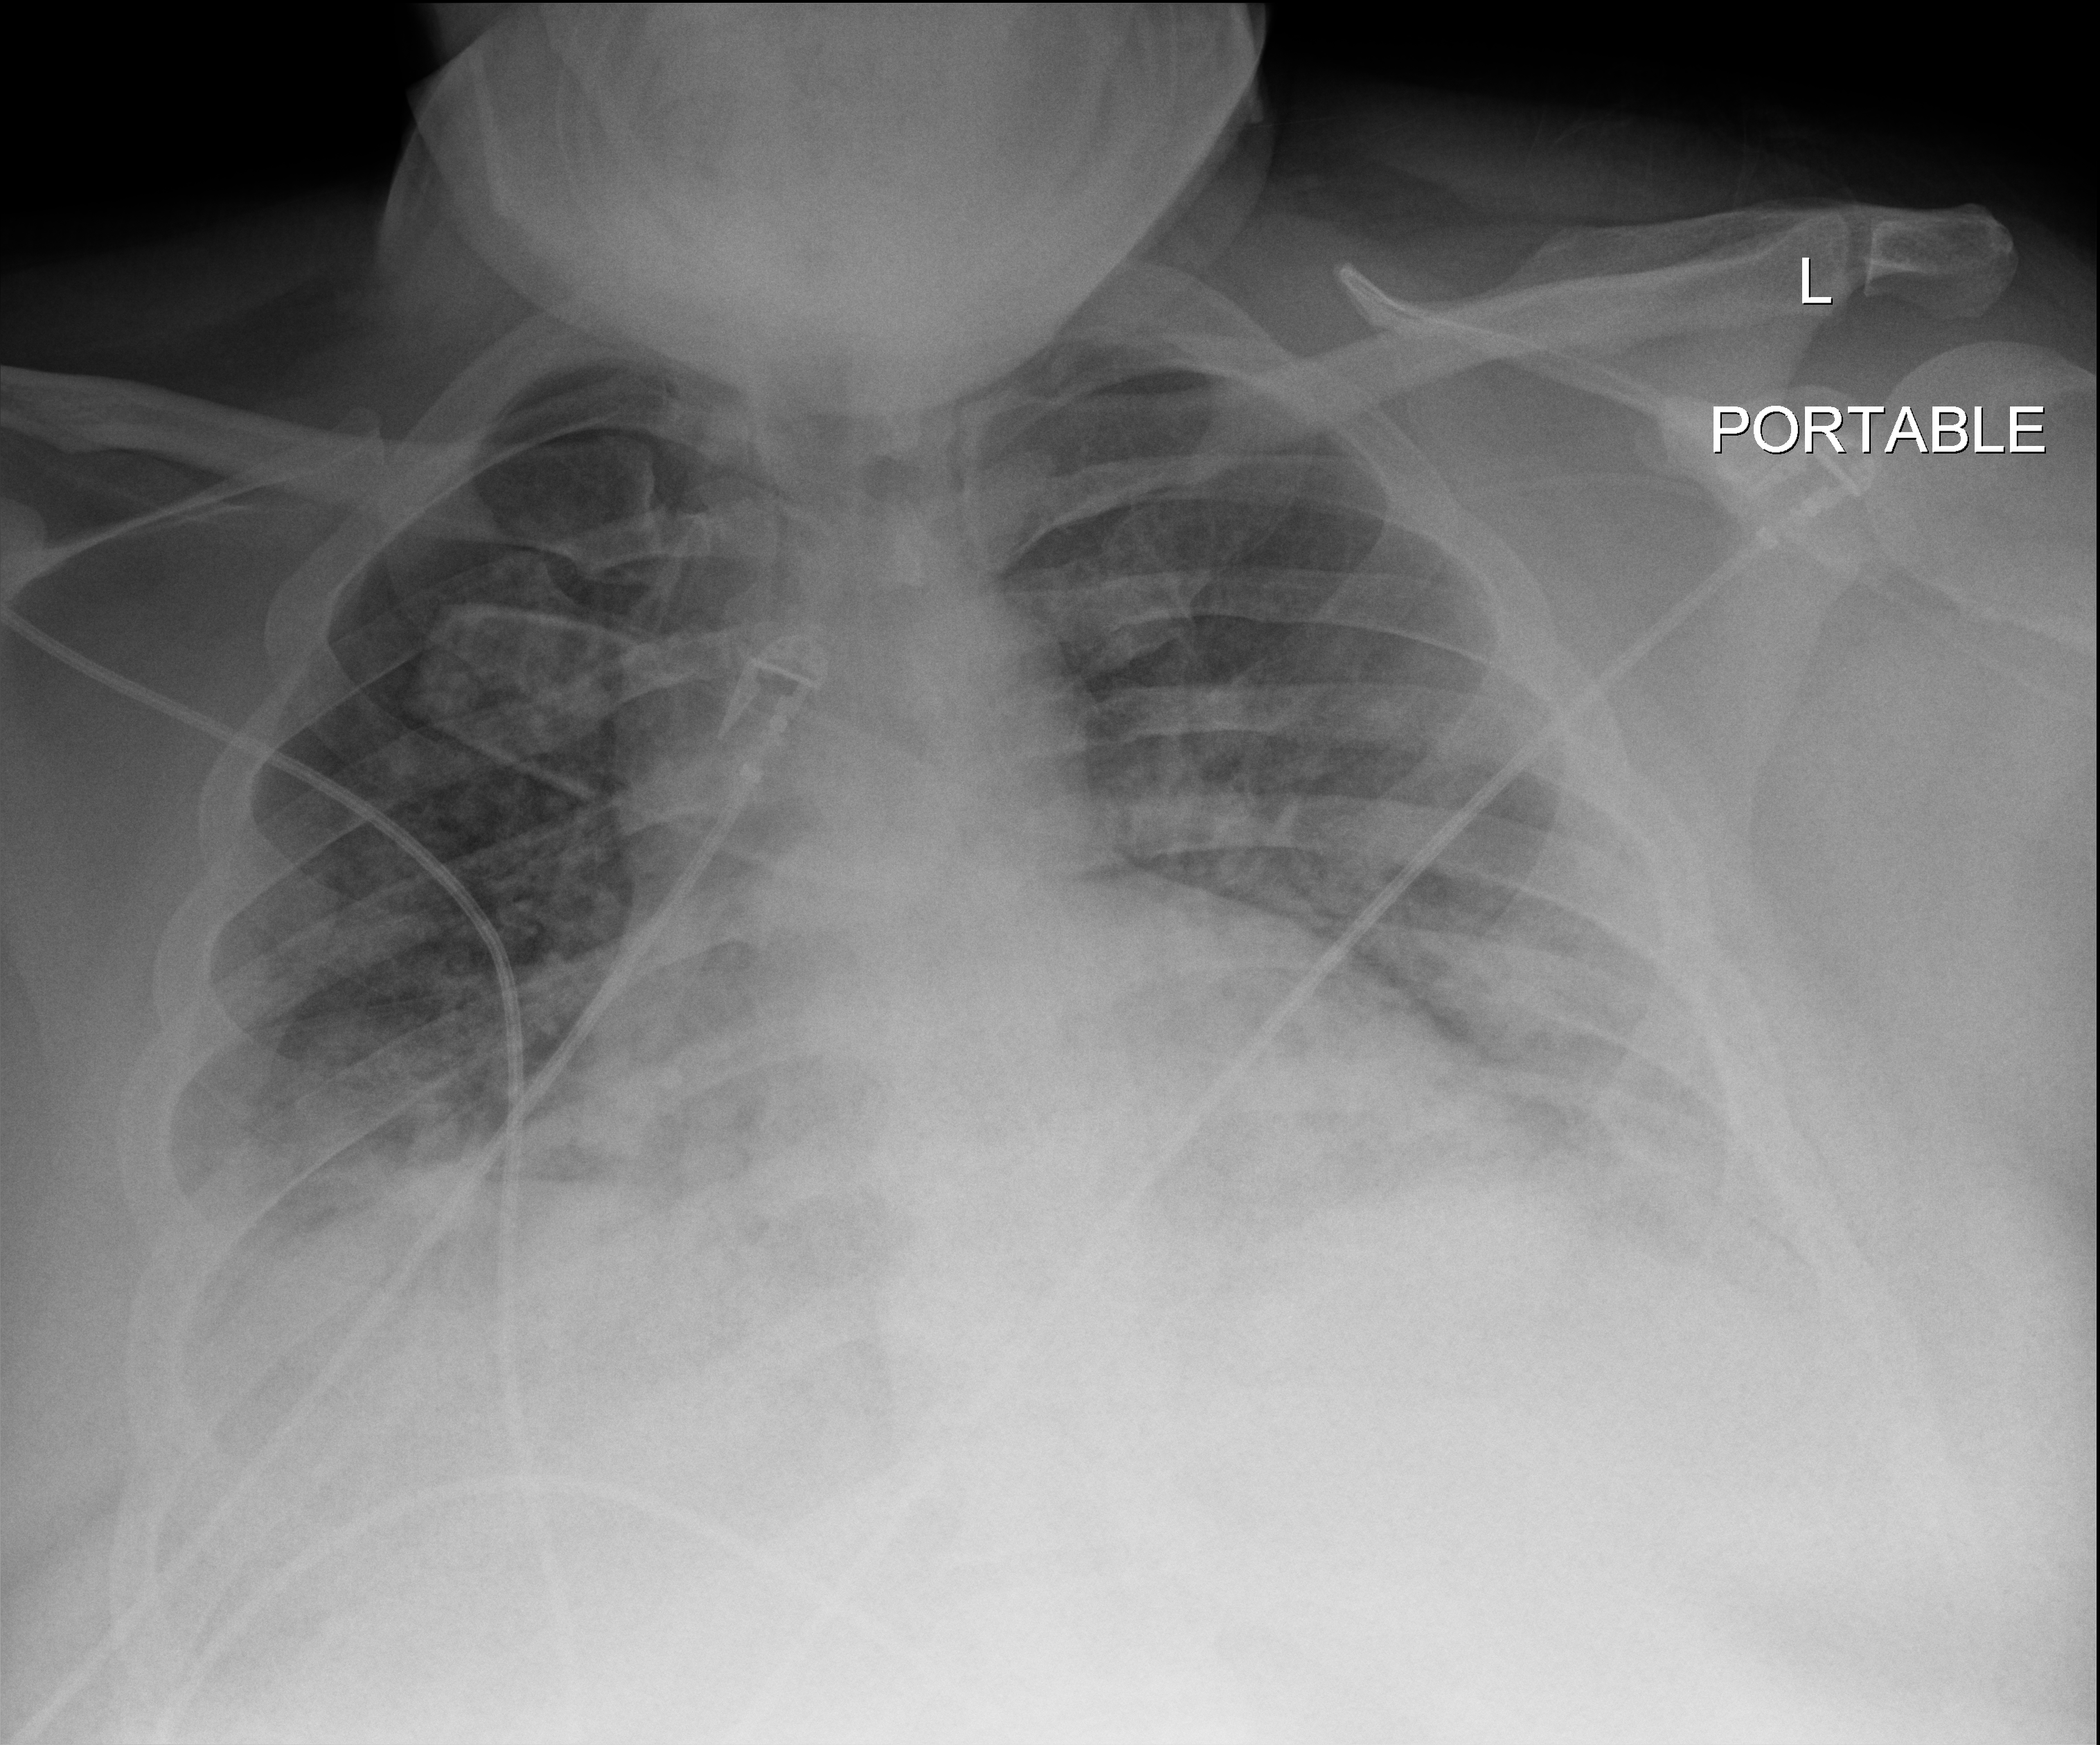
Portable chest radiograph; anteroposterior (AP) projection. Male patient hospitalised with COVID-19, age 18–59 years.
From the hospital-stay record, not from the radiograph (when in the stay this image was taken is not recorded): diabetes (admission record): yes; mechanically ventilated during this hospital stay: no; admitted to intensive care during this hospital stay: yes.